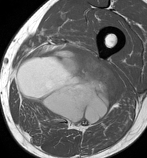
MRI of an extremity soft-tissue mass, one axial slice; slice 54 of 86 in the series (ordered by position); MR volume resampled by the dataset authors to the PET/CT grid (not the native acquisition matrix); 3.27 mm slice thickness; 147 × 158 image matrix. Male patient. From the clinical record (not read from this slice): histological type: undifferentiated pleomorphic liposarcoma; grade: high; site of the primary tumour: left thigh.
Annotated regions visible in this slice (expert contour drawn on MRI and transferred to this co-registered scan by the dataset authors):
- gross tumour volume including surrounding oedema: bounding box <16,47,120,130> (left, top, right, bottom; pixels)
- gross tumour volume (mass): <16,47,120,128>